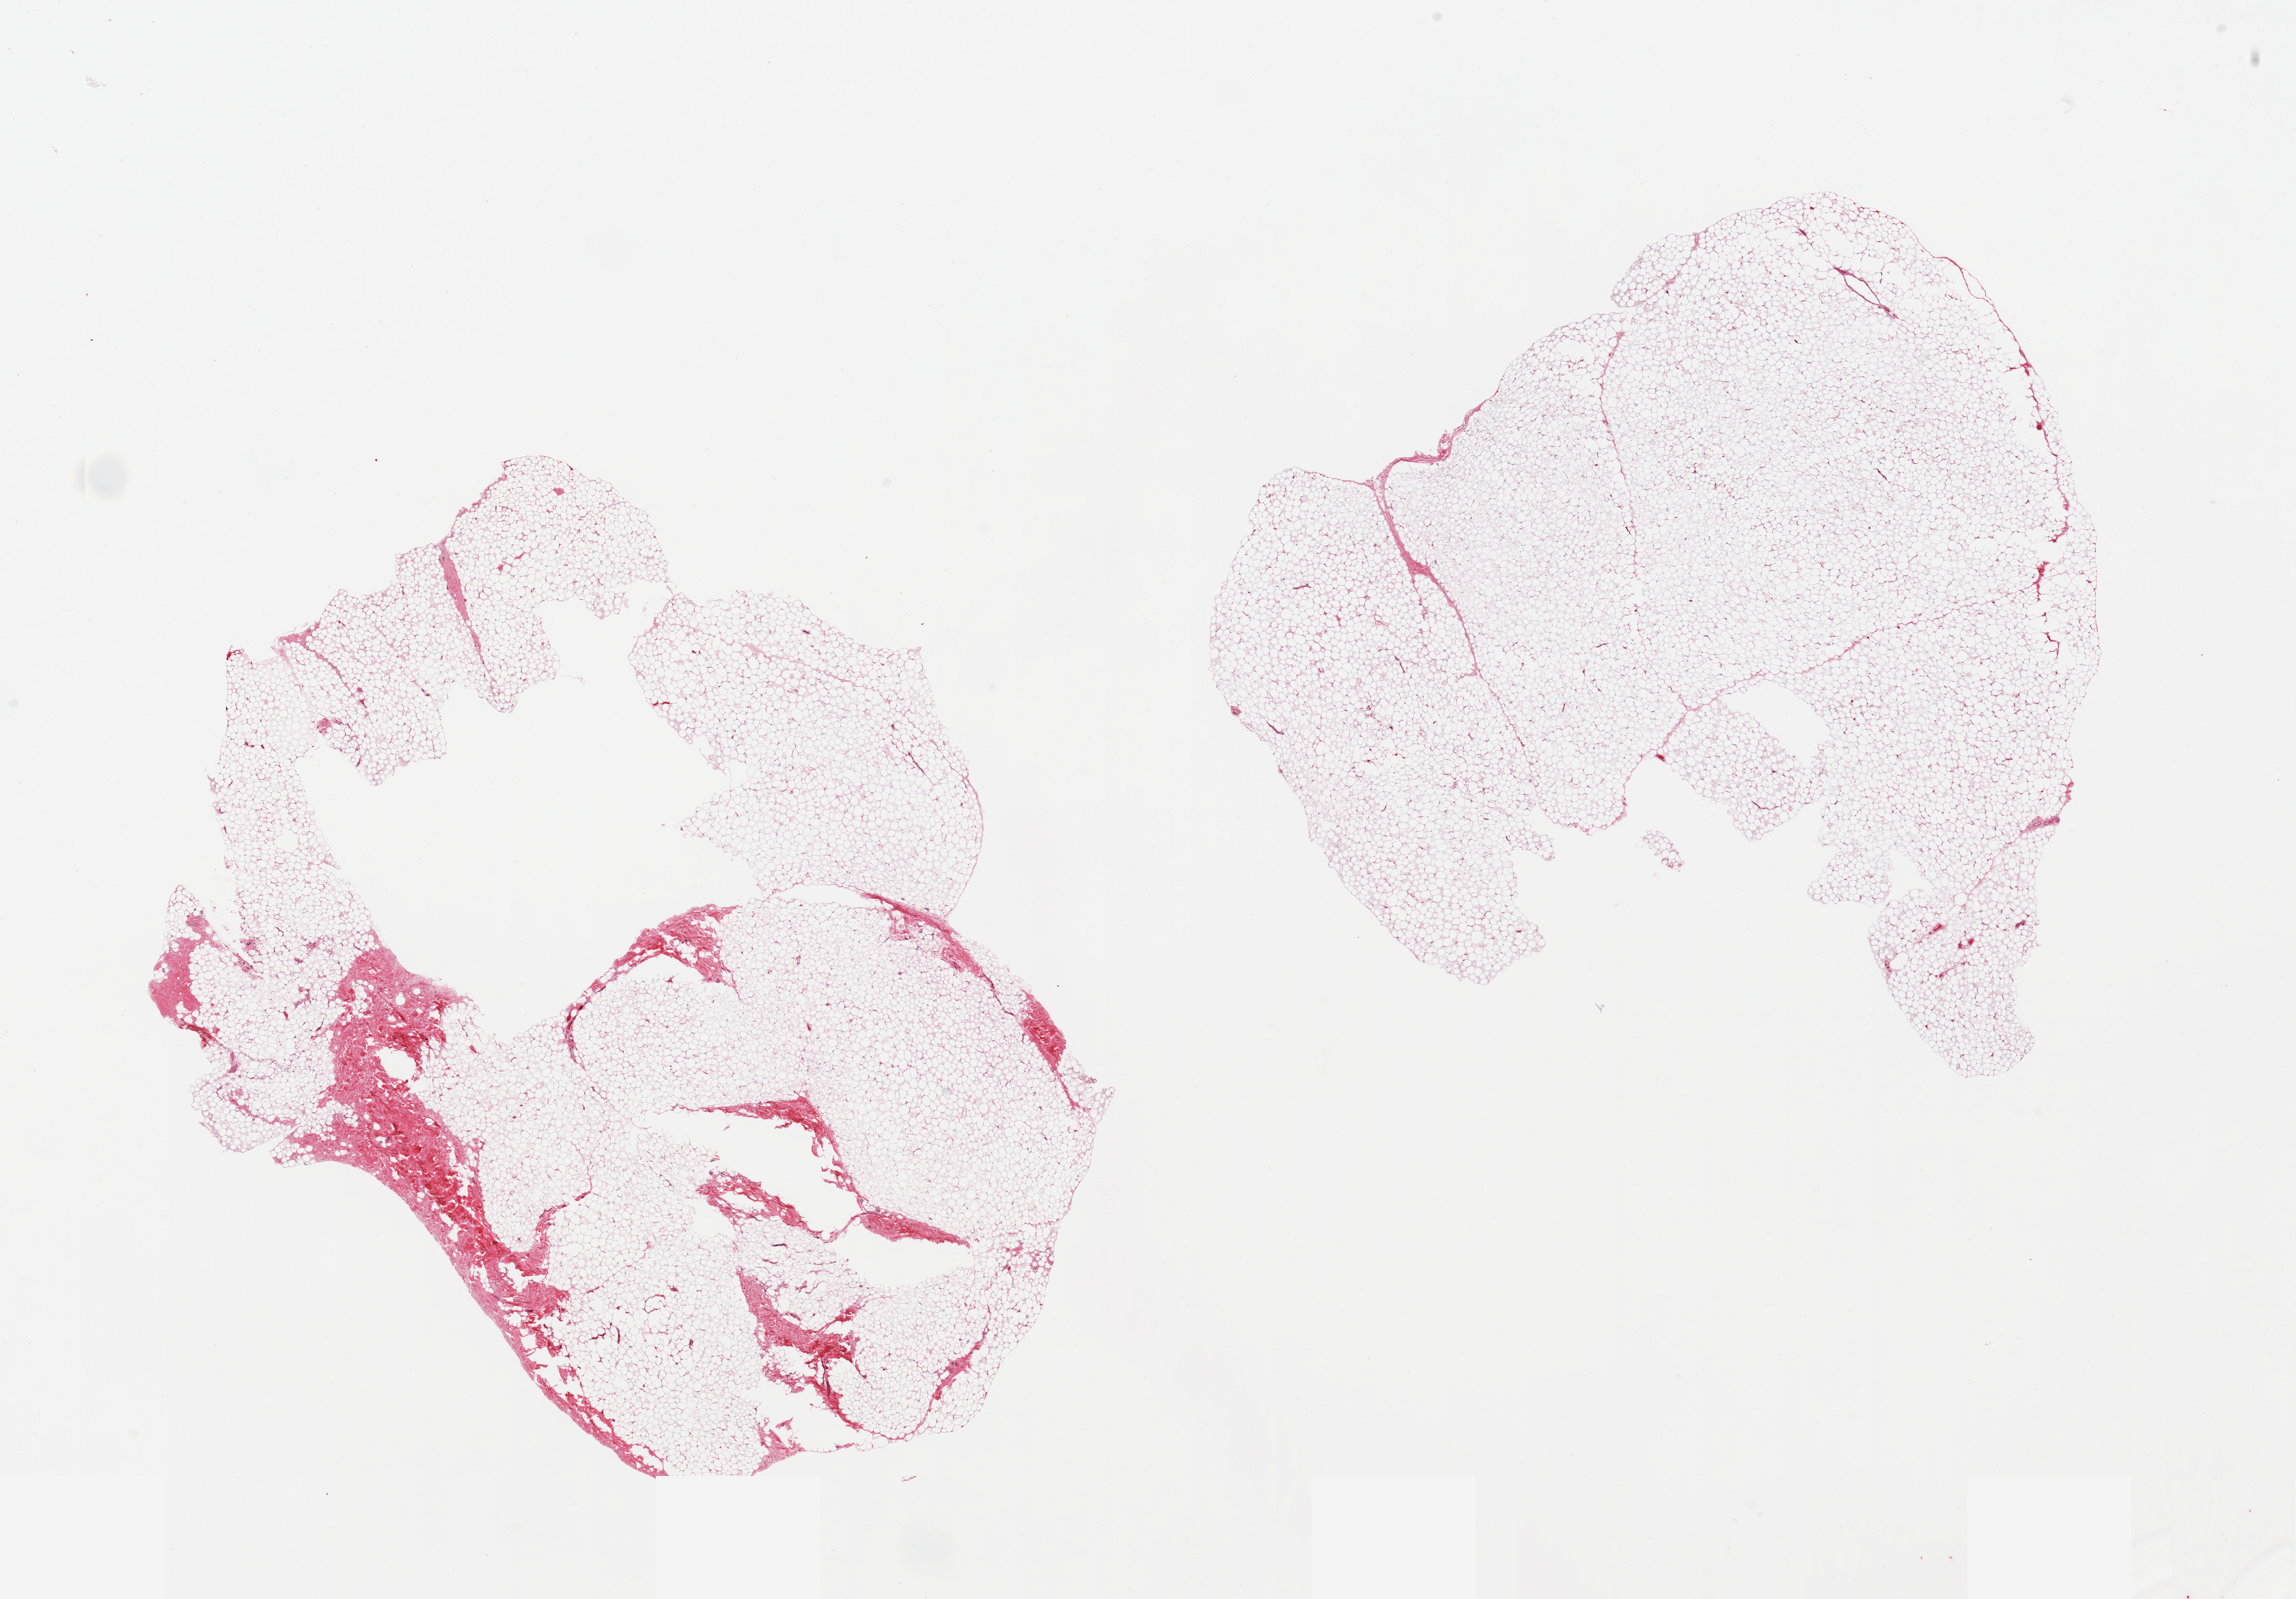
Haematoxylin and eosin whole-slide image, brightfield, whole scanned area (about 26.6 x 18.5 mm, slide scanned at 20x) shown as a low-resolution overview, PAXgene-fixed, paraffin-embedded tissue, target tissue: breast, tissue donor sample. Male donor.
Review note (as recorded): 2 pieces; central defect in one piece, predominantly fat with ~10% fibrous tissue in one piece, no epithelial component.